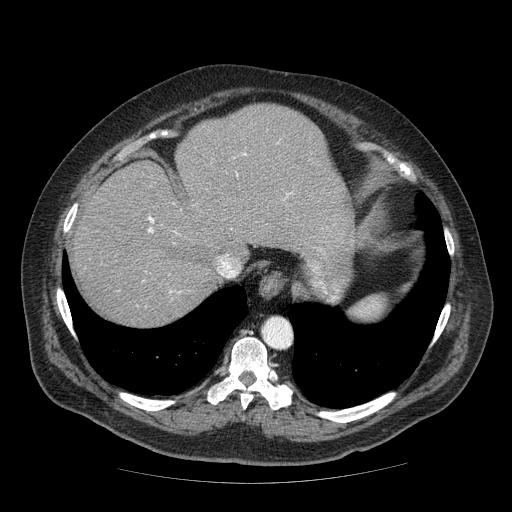
Contrast-enhanced abdominal CT (liver protocol), one axial slice. Slice 55 of 85 in the series (ordered by position). 120 kVp. Soft-tissue window (W 400 / L 40 HU). 2.5 mm slice thickness. 512 × 512 image matrix. From the clinical record (not read from this slice): diagnosis: hepatocellular carcinoma (patient treated with transarterial chemoembolisation; whether this scan precedes or follows treatment is not stated here); TNM stage (as recorded): Stage-IIIA.
Outlined on this slice (semi-automatic segmentation, software-assisted and operator-edited):
- abdominal aorta: bounding box [x1, y1, x2, y2] px = [263, 319, 292, 349]
- liver parenchyma outside the tumour (the mass and vessels are separate outlines, so this box may not span the whole liver): [72, 104, 354, 326]
- liver vessels: [148, 153, 289, 292]